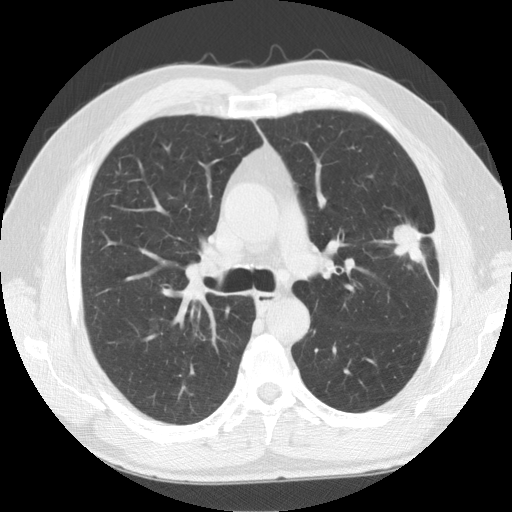
Chest CT (low-dose screening protocol), one axial image; baseline screening round; lung window (W 1500 / L -600 HU); 2.5 mm slice thickness; standard (soft-tissue) reconstruction kernel (STANDARD); 512 × 512 image matrix, field of view 360 × 360 mm. Male participant, aged 59 years at enrolment.
Expert-annotated lung lesion, bounding box <373,204,454,283> (left, top, right, bottom; pixels). The exam's reader record, not a measurement of the box and not confirmed to be the same lesion: non-calcified nodule or mass ≥4 mm, left upper lobe, 23 × 23 mm, spiculated (stellate) margins, soft tissue attenuation. Later outcome: lung cancer diagnosed 28 days after this screen — squamous cell carcinoma, NOS, left upper lobe, moderately differentiated (G2), stage IA (AJCC 6th edition), 27 mm at pathology.